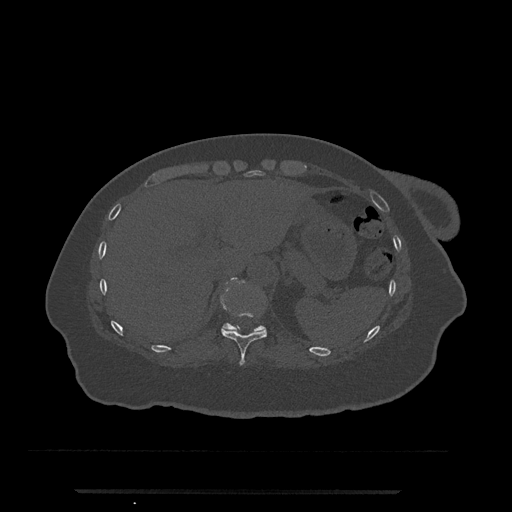
CT including the spine, one axial slice; 120 kVp; bone window (W 1800 / L 400 HU); 0.5 mm slice thickness; 512 × 512 image matrix. Patient: female, 51 years. Case-level facts recorded for this patient, not image findings: primary cancer: neuro; vertebrae with lytic lesions (as recorded): T8.
Annotated regions visible in this slice (semi-automatic segmentation, software-assisted and operator-edited):
- T10 vertebra: box from (x=220, y=280) to (x=267, y=365) px
- T11 vertebra: (x=223, y=323)–(x=264, y=331)